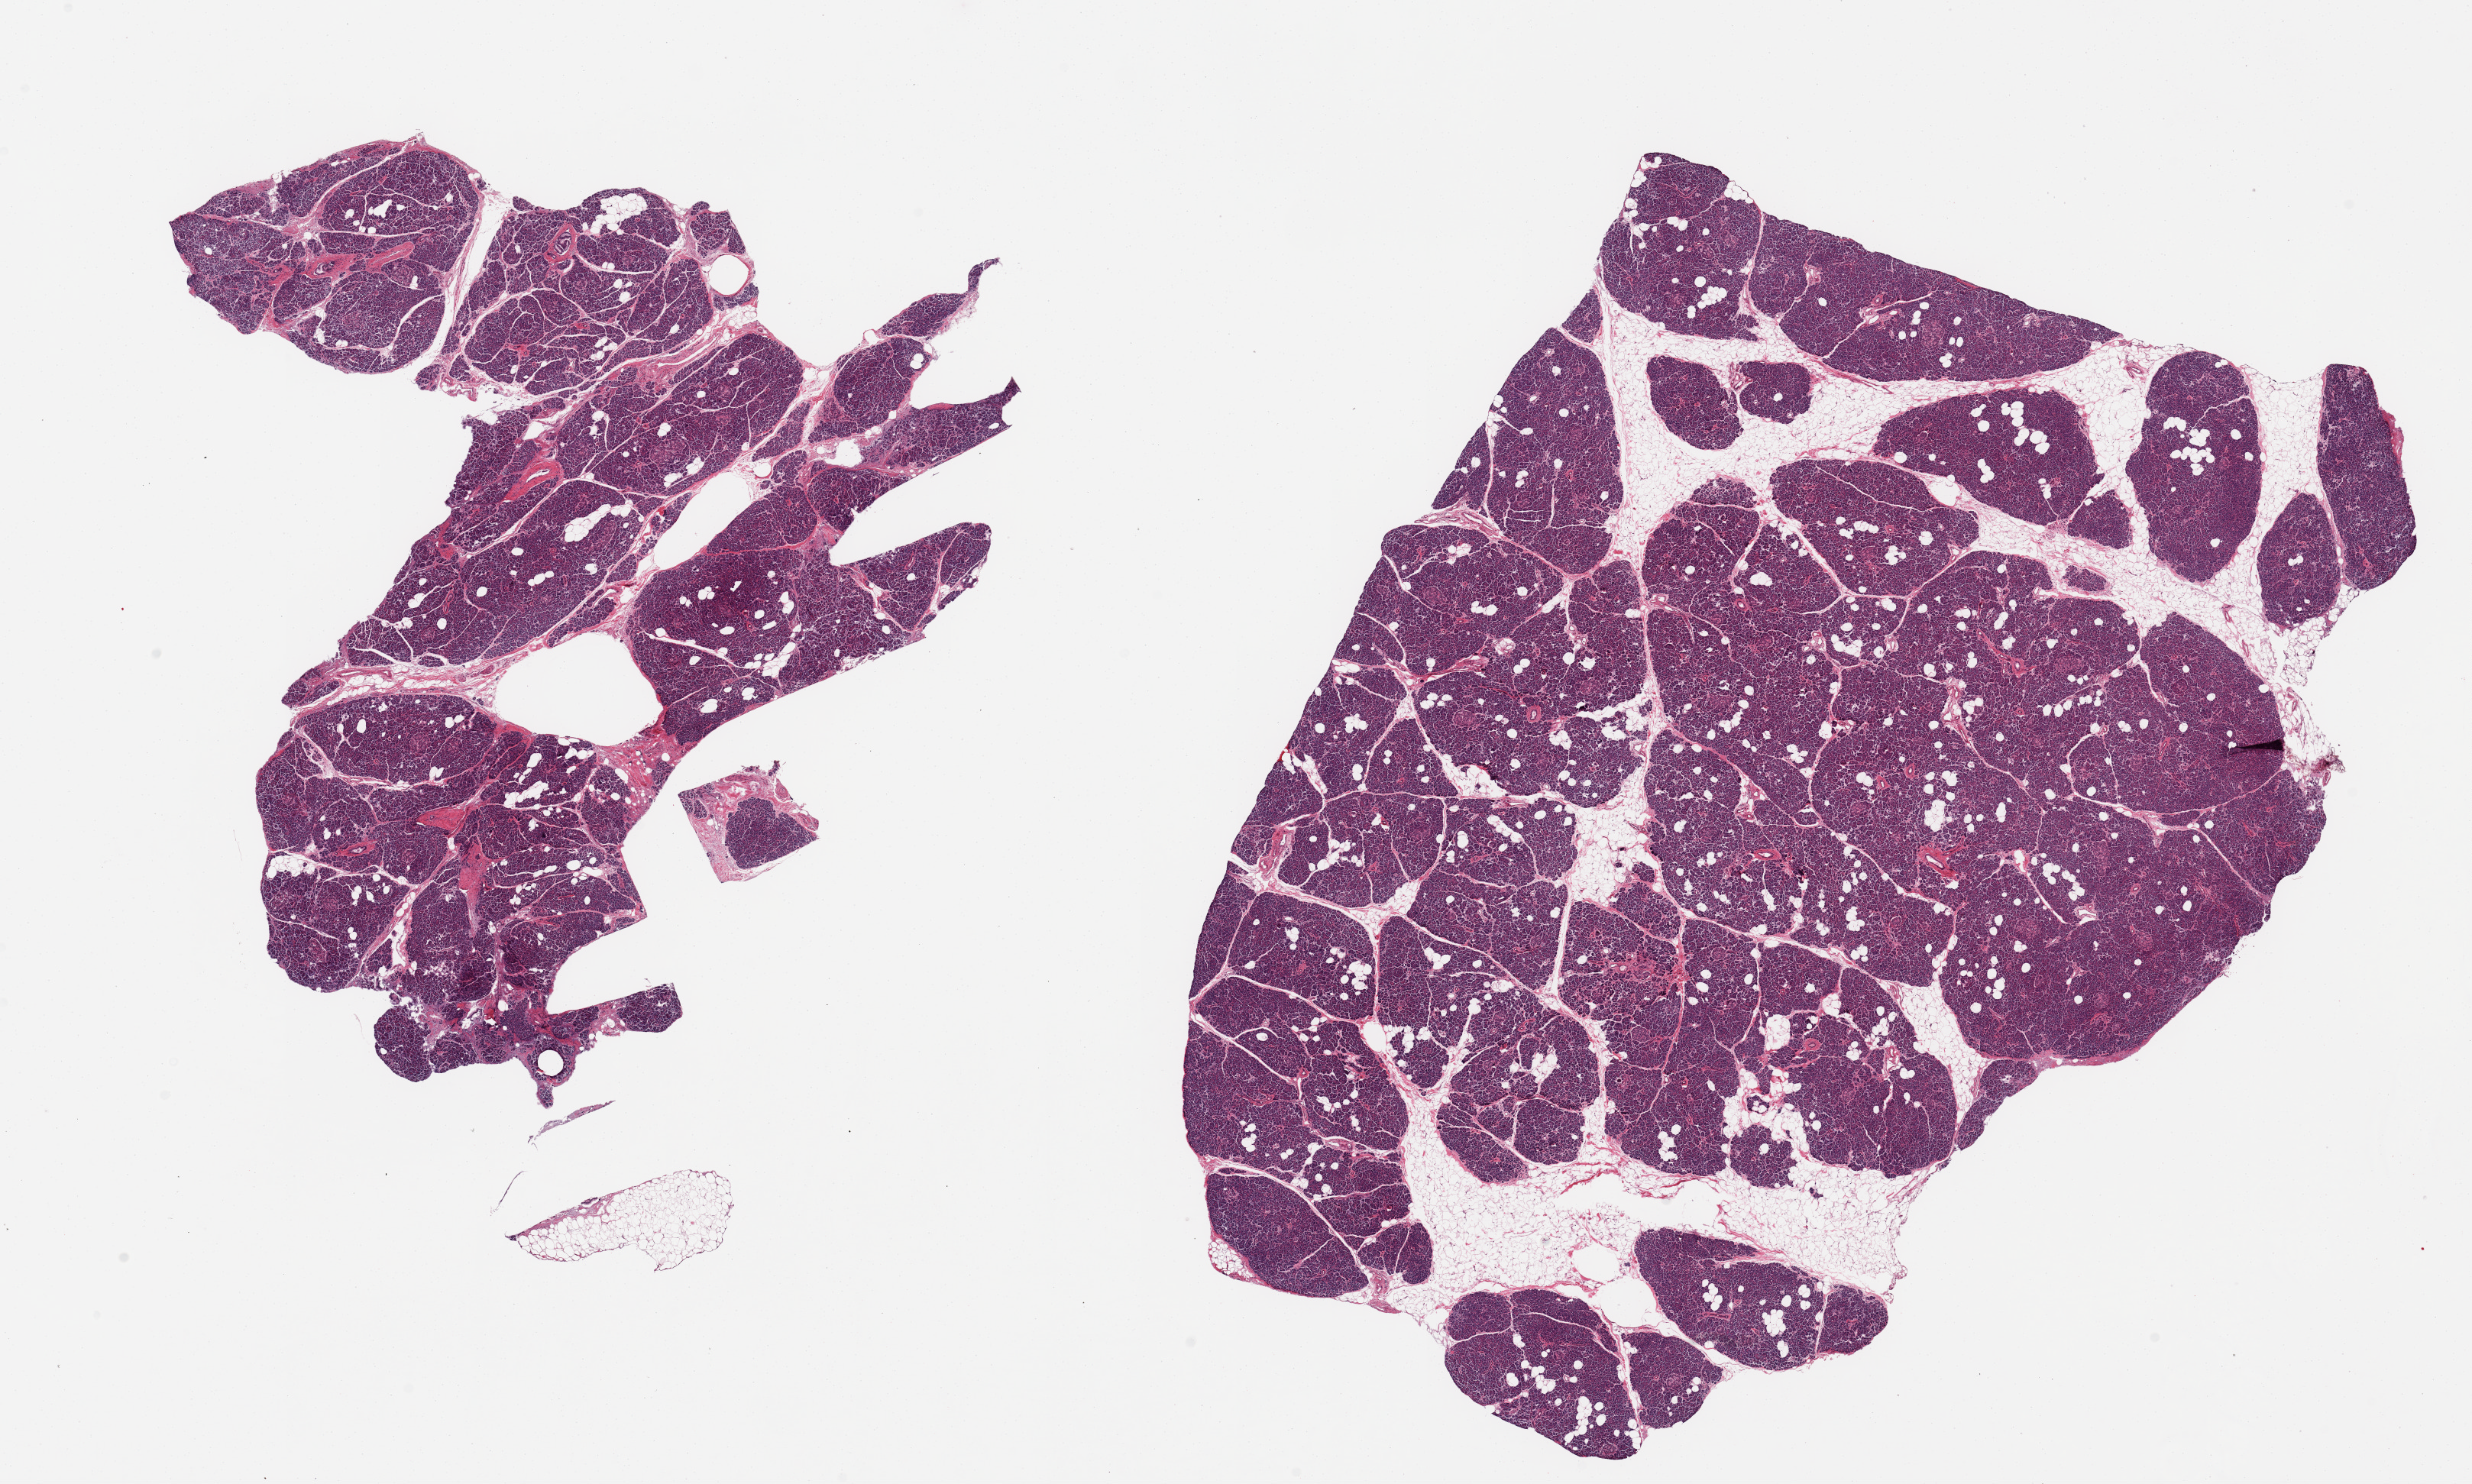
Digitized haematoxylin and eosin-stained section, whole scanned area (about 25.6 x 15.4 mm) shown as a low-resolution overview; PAXgene-fixed, paraffin-embedded tissue; target tissue: pancreas; tissue donor sample. Female donor.
* review note (as recorded): 2 pieces, Islets well preserved